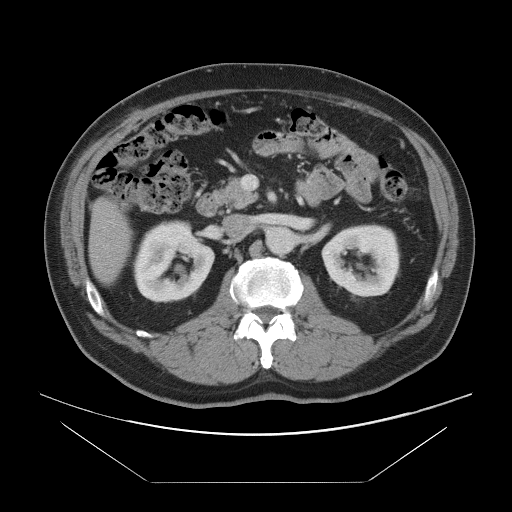
Contrast-enhanced abdominal CT, one axial slice; slice 39 of 97 in the series (ordered by position); intravenous contrast given; soft-tissue window (W 400 / L 40 HU); 512 × 512 image matrix, field of view 442 × 442 mm. Male patient, age 62 years. From the clinical record (not read from this slice): diagnosis: colorectal cancer liver metastases, imaged before liver resection; multiple liver metastases: no; largest metastasis: 7 cm; disease in both lobes: yes.
Annotated regions visible in this slice (outlined manually by an expert reader):
- liver: box from (x=90, y=200) to (x=130, y=282) px
- planned liver remnant (the part of the liver to remain after resection): (x=91, y=200)–(x=130, y=282)